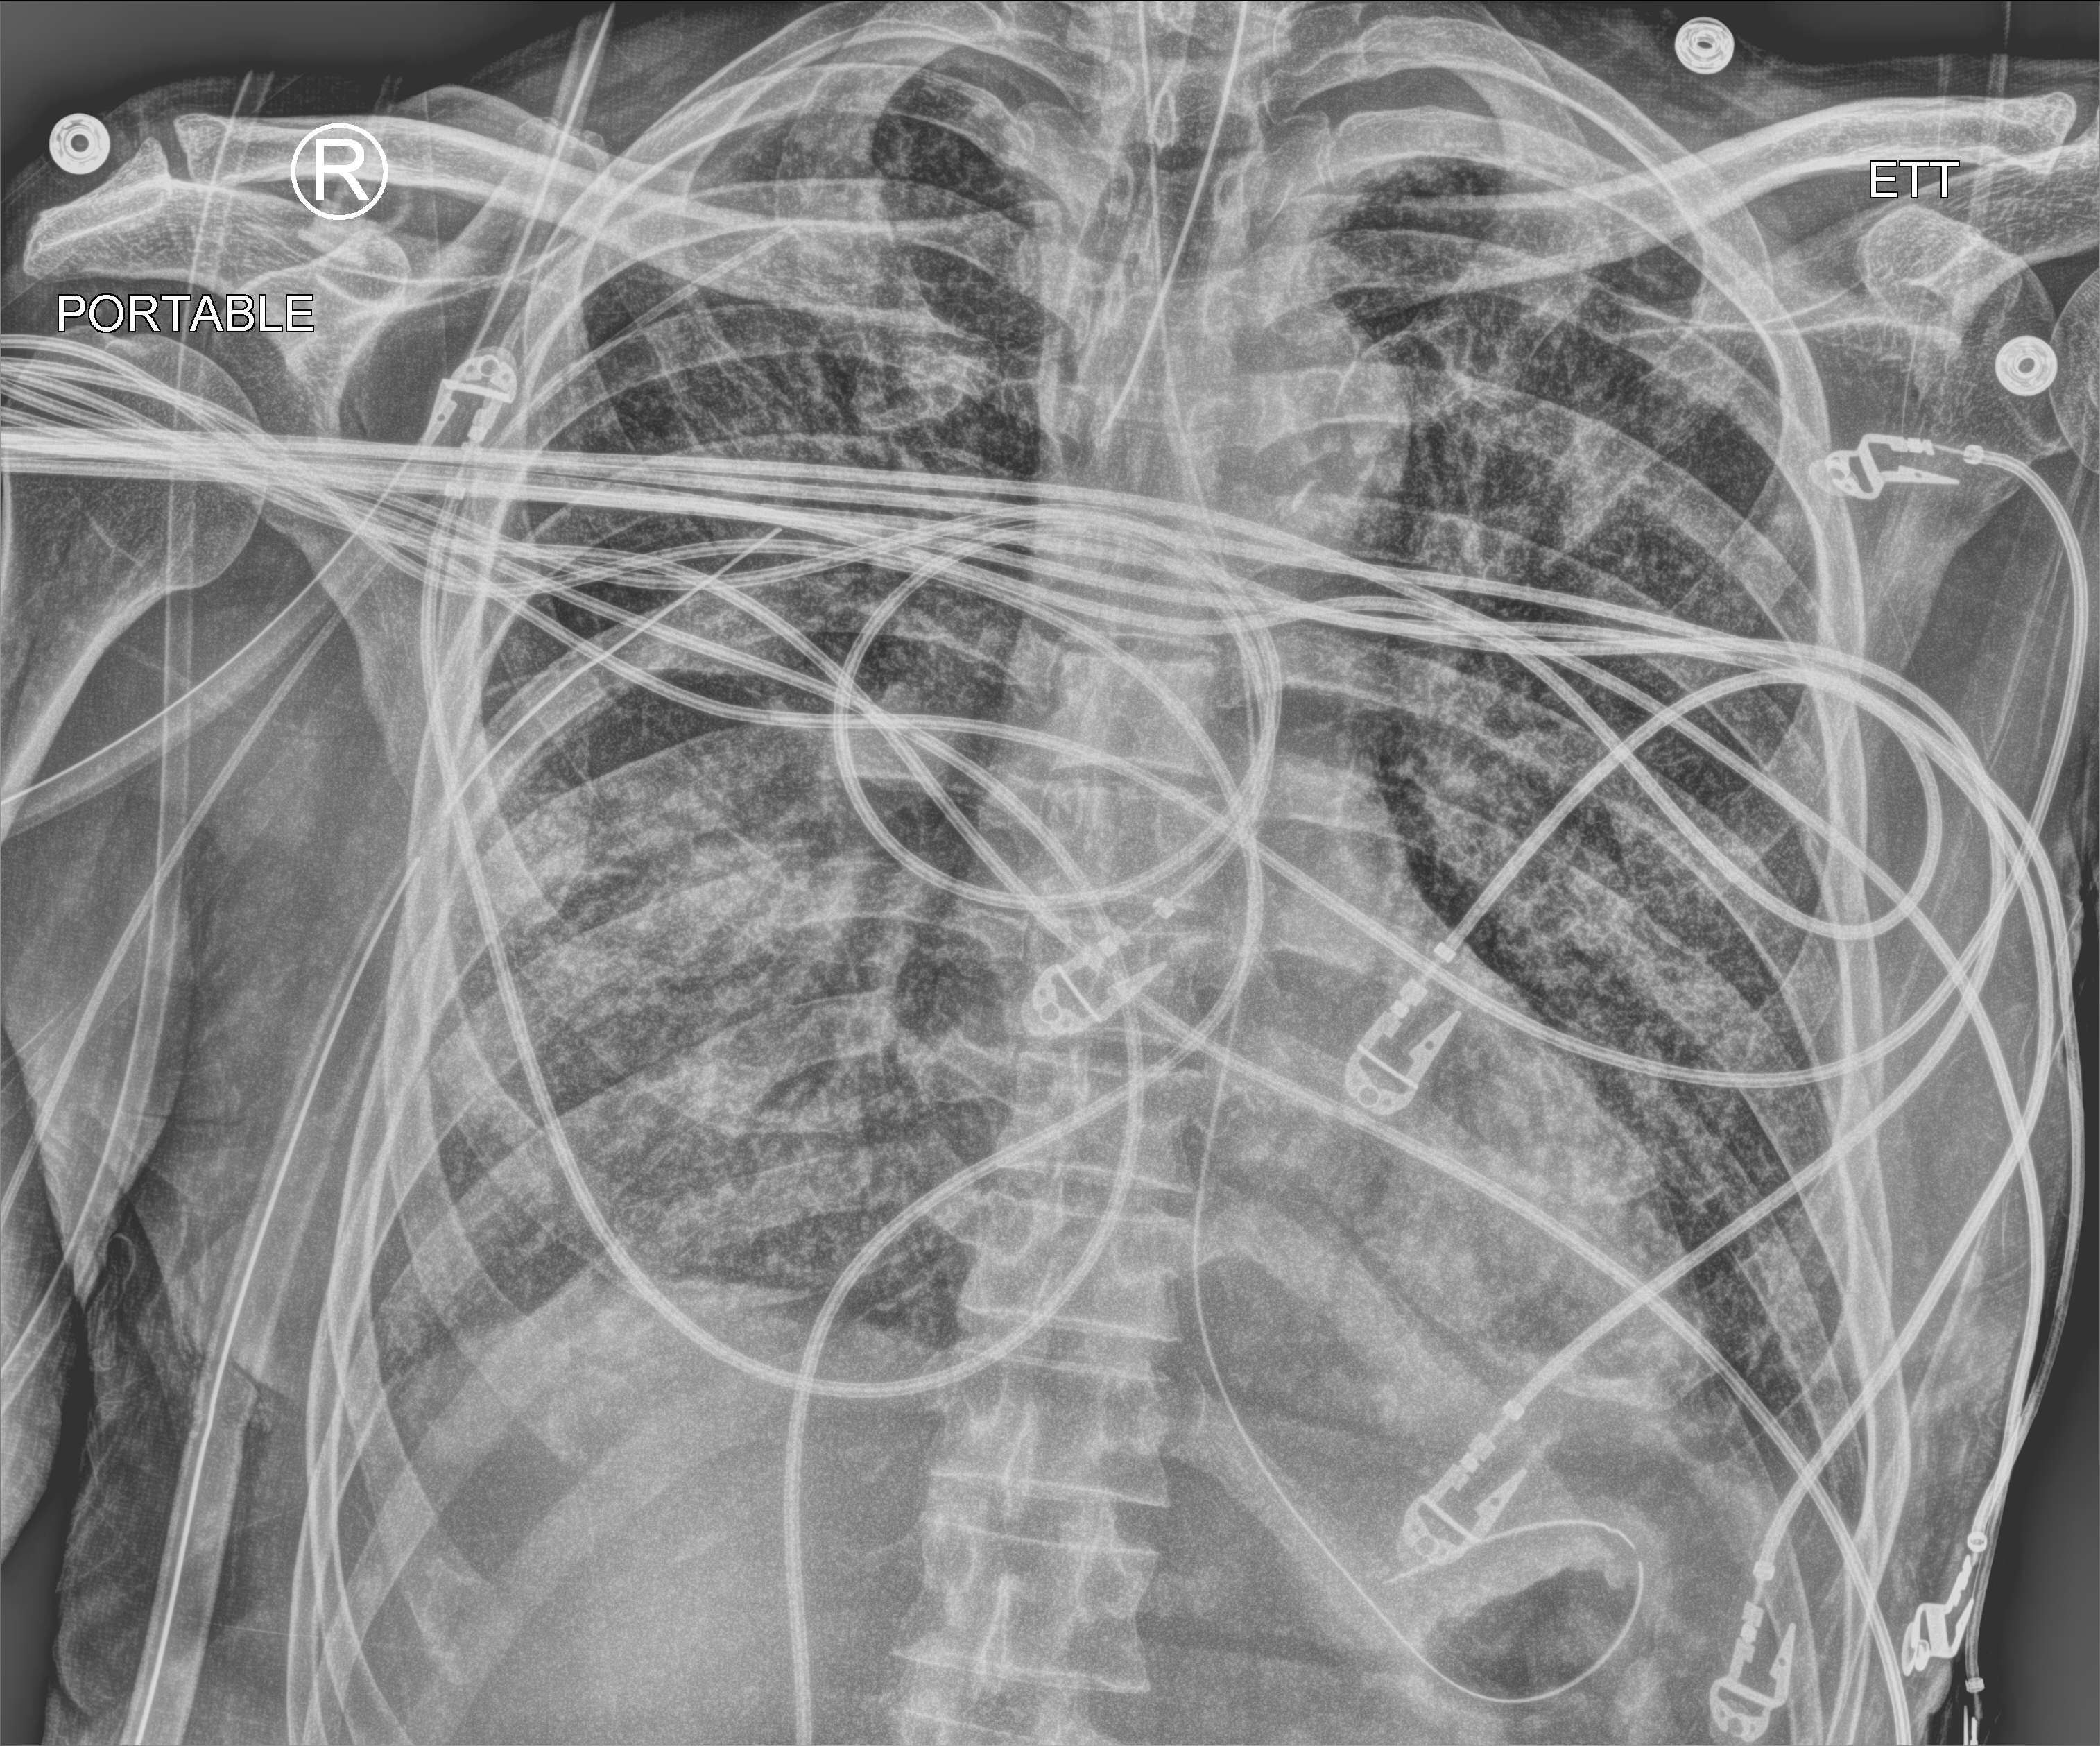
Bedside chest radiograph (computed radiography), anteroposterior (AP) projection. Patient hospitalised with COVID-19; male, aged 60–74 years.
Hospital-stay facts (about this admission, not read from this image; timing relative to this image not recorded):
- length of hospital stay: 31 days